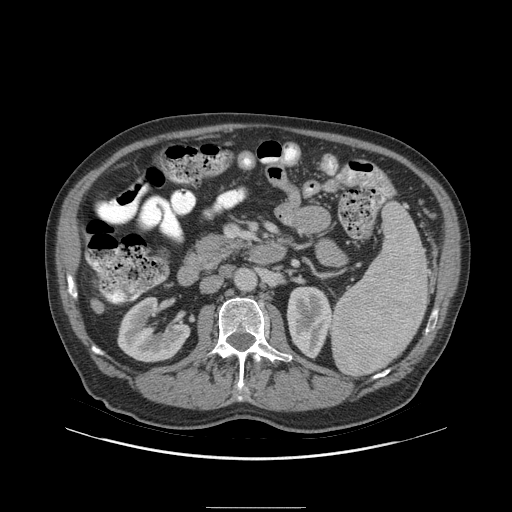
Contrast-enhanced abdominal CT (liver protocol), one axial slice. Reconstruction kernel STANDARD. 140 kVp. Soft-tissue window (W 400 / L 40 HU). 2.5 mm slice thickness. 512 × 512 image matrix, field of view 440 × 440 mm. From the clinical record (not read from this slice): diagnosis: hepatocellular carcinoma (patient treated with transarterial chemoembolisation; whether this scan precedes or follows treatment is not stated here); TNM stage (as recorded): Stage-I; Child-Pugh class: A; tumour size: 5.1 cm.
Outlined on this slice (semi-automatic segmentation, software-assisted and operator-edited):
- liver parenchyma outside the tumour (the mass and vessels are separate outlines, so this box may not span the whole liver): bounding box [x1, y1, x2, y2] px = [92, 300, 102, 312]